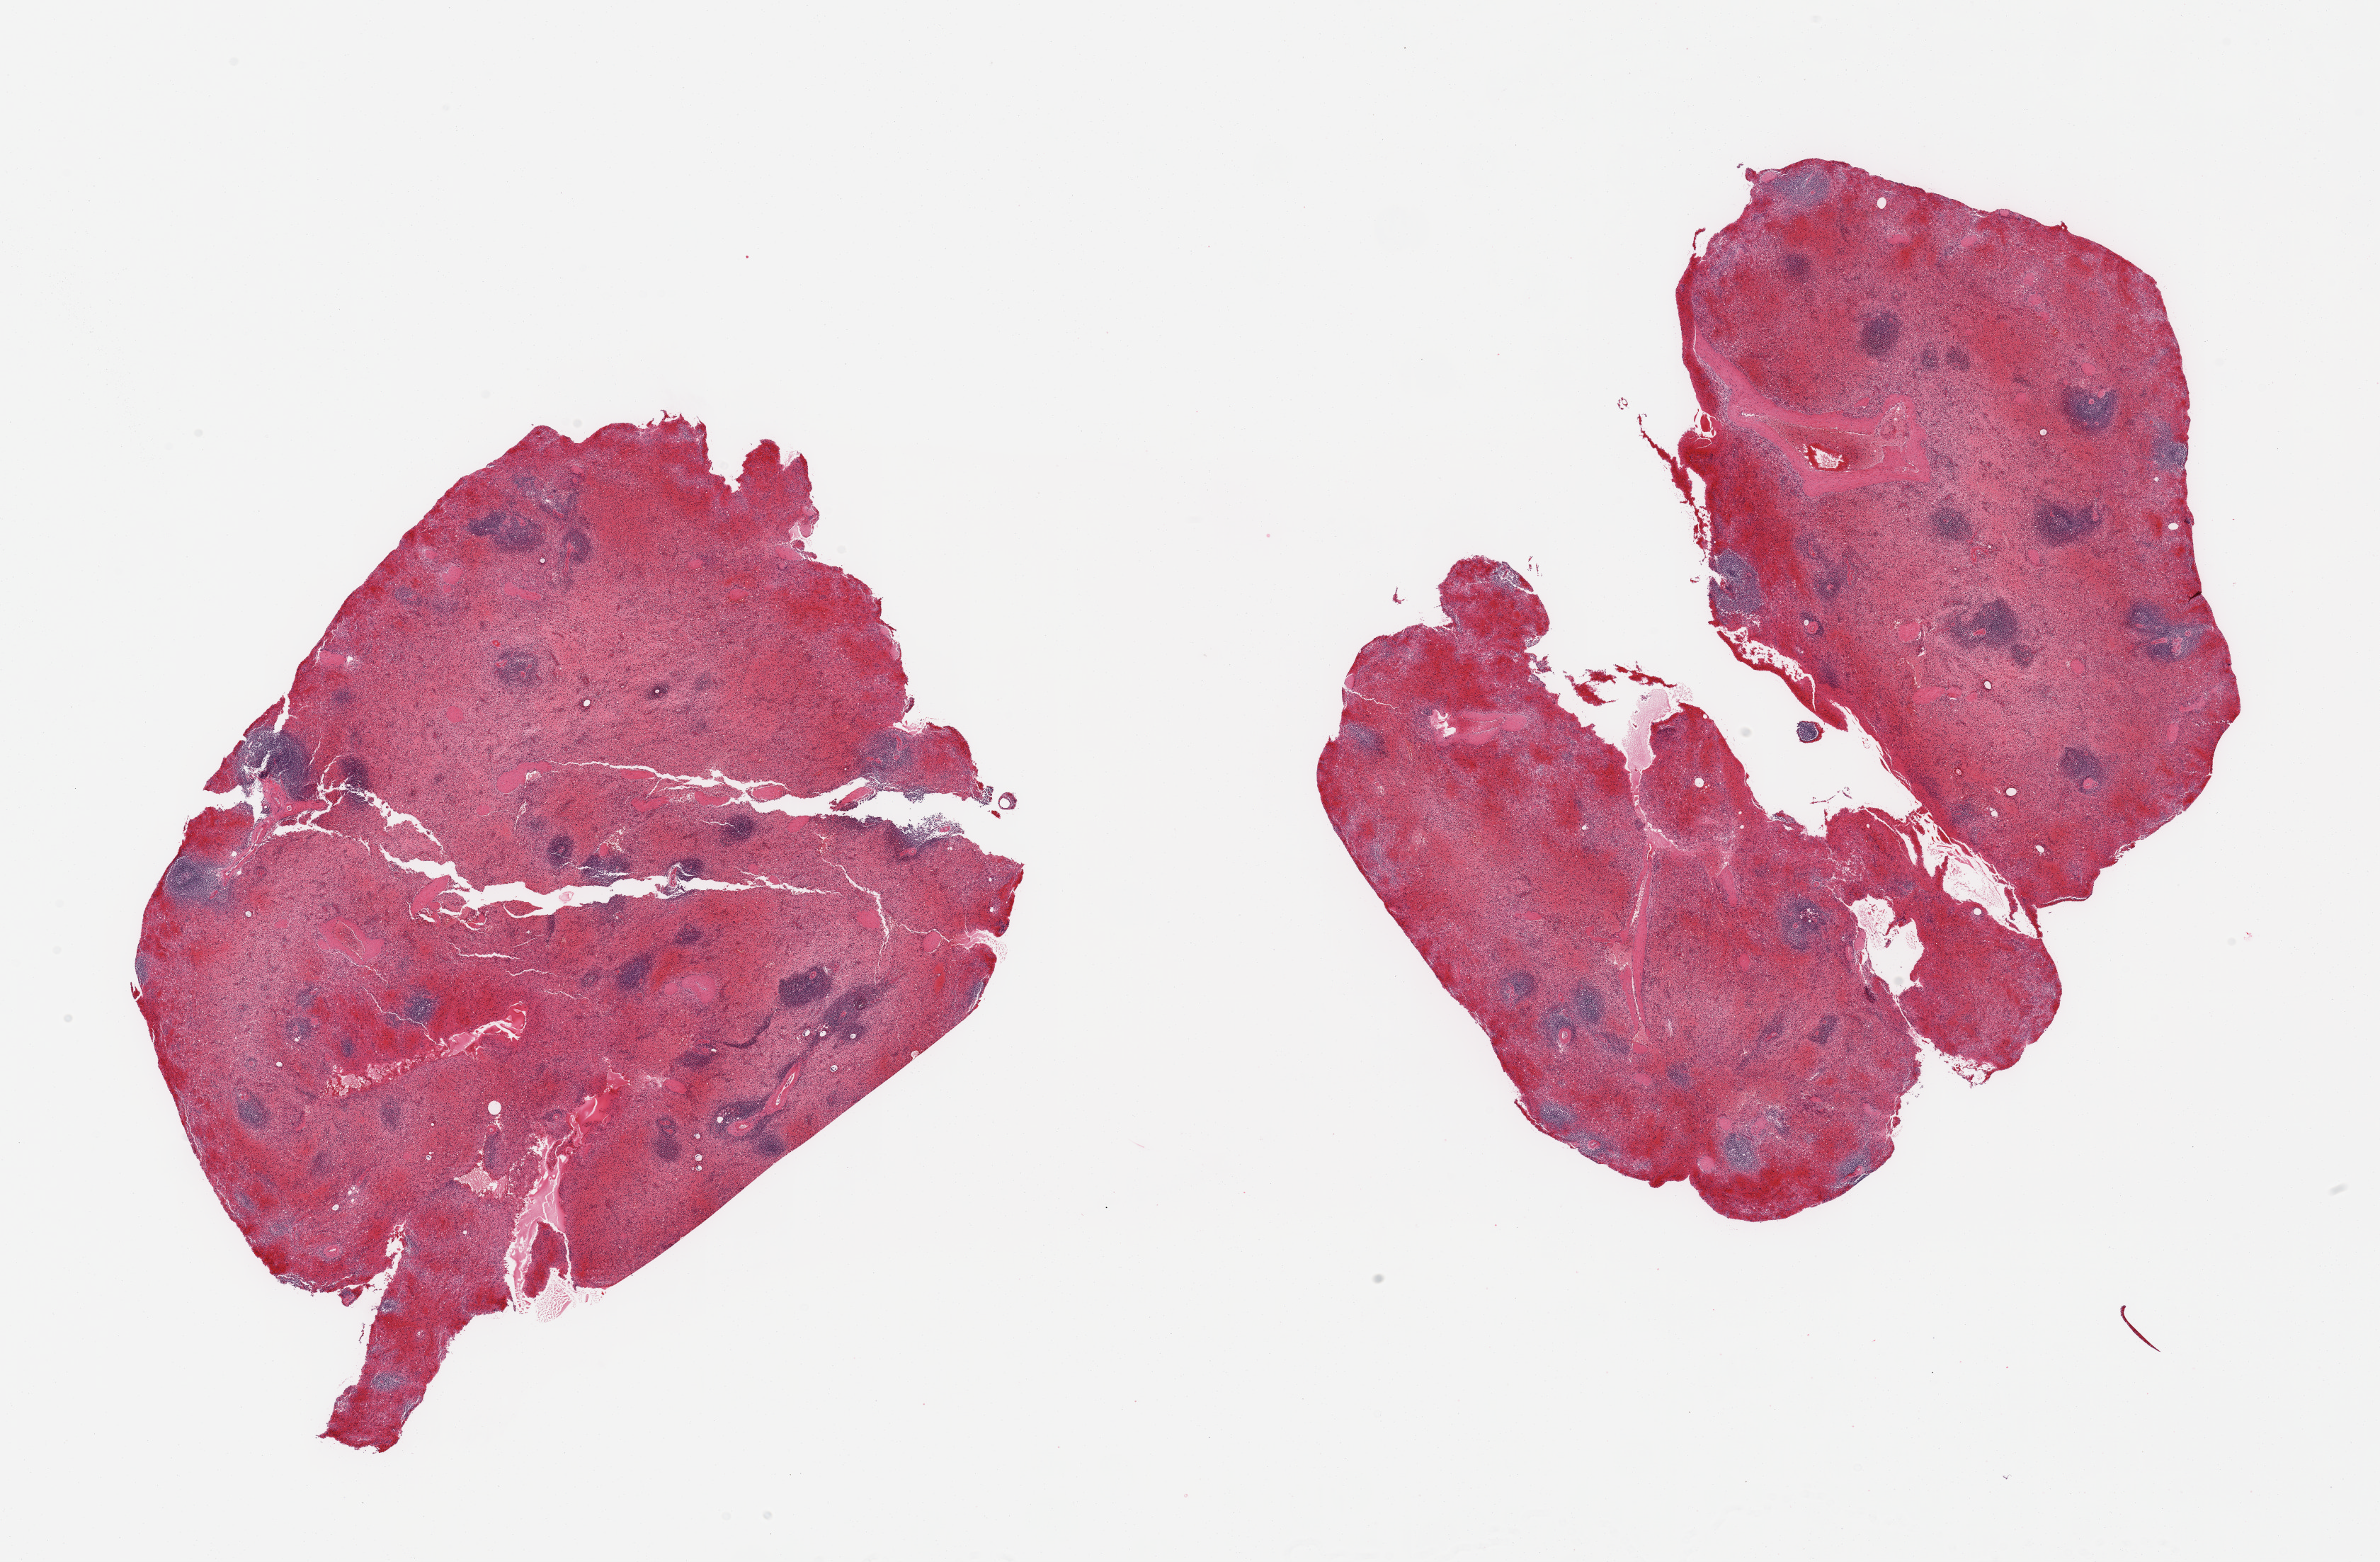
Hematoxylin and eosin (H&E) whole-slide image, low-resolution overview of the scanned area, about 26.6 x 17.4 mm, PAXgene-fixed paraffin-embedded (PFPE) section, section of spleen (target tissue), donor tissue sample.
Reviewer comment on this tissue sample: 2 pieces; congested.